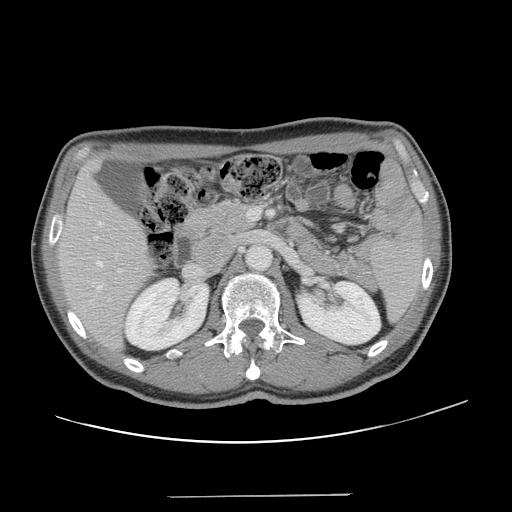
Contrast-enhanced abdominal CT, one axial slice; intravenous contrast given; soft-tissue window (W 400 / L 40 HU); 2.5 mm slice thickness; 512 × 512 image matrix, field of view 403 × 403 mm. Male patient, age 60 years. From the clinical record (not read from this slice): diagnosis: colorectal cancer liver metastases, imaged before liver resection; multiple liver metastases: no; largest metastasis: 2.5 cm; chemotherapy before resection: no.
Outlined on this slice (expert manual segmentation):
- hepatic veins: bounding box <97,222,102,290> (left, top, right, bottom; pixels)
- liver: <59,164,155,349>
- planned liver remnant (the part of the liver to remain after resection): <59,163,154,349>